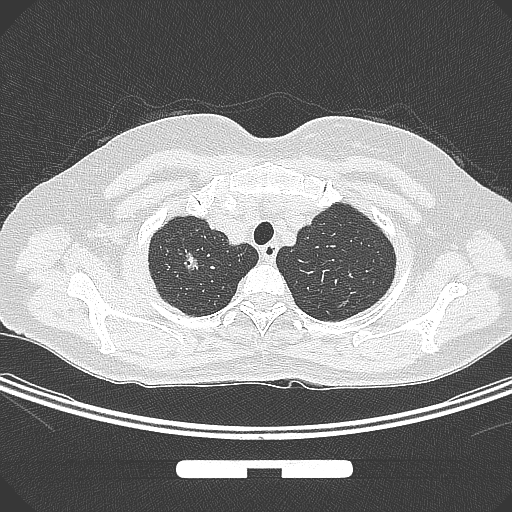
Chest CT, one axial slice. Position 256 of 295 along the scan axis. 120 kVp. Lung window (W 1500 / L -600 HU). 1 mm slice thickness. 512 × 512 image matrix. Female patient, age 58 years. Case-level facts recorded for this patient, not image findings: clinical TNM (as recorded): T1b N0 M0; histopathological grade: G2-3.
Structures marked on this image (rectangle marked by the reading radiologist):
- lung tumour (recorded histology: adenocarcinoma): box from (x=175, y=245) to (x=207, y=278) px